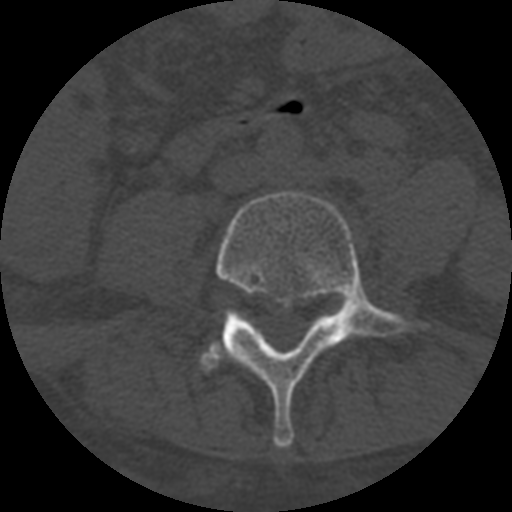
CT including the spine, one axial slice. Slice 206 of 708 in the series (ordered by position). 120 kVp. One of 3 acquisitions stored at this slice position. Bone window (W 1800 / L 400 HU). 1.25 mm slice thickness. 512 × 512 image matrix, field of view 160 × 160 mm. Patient age 55 years. From the clinical record (not read from this slice): primary cancer: colon.
Outlined on this slice (semi-automatic segmentation, software-assisted and operator-edited):
- L4 vertebra: bounding box (x1, y1, x2, y2) in pixels: (192, 191, 423, 448)